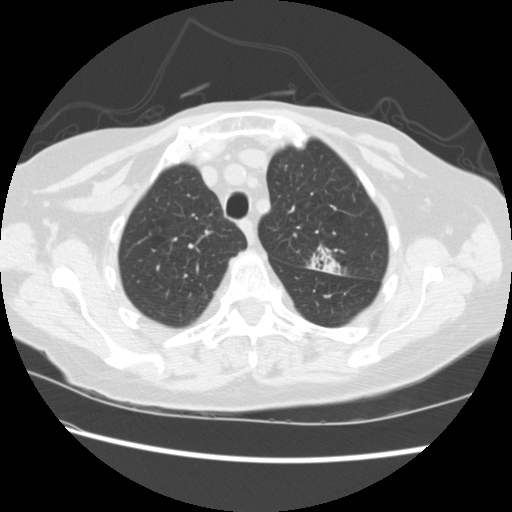
Low-dose screening chest CT, one axial slice. Lung window (W 1500 / L -600 HU). 512 × 512 image matrix, field of view 340 × 340 mm.
Annotated regions visible in this slice (expert manual segmentation):
- lesion 1 (tumor, upper lobe of left lung): bounding box (x1, y1, x2, y2) in pixels: (308, 246, 342, 275)